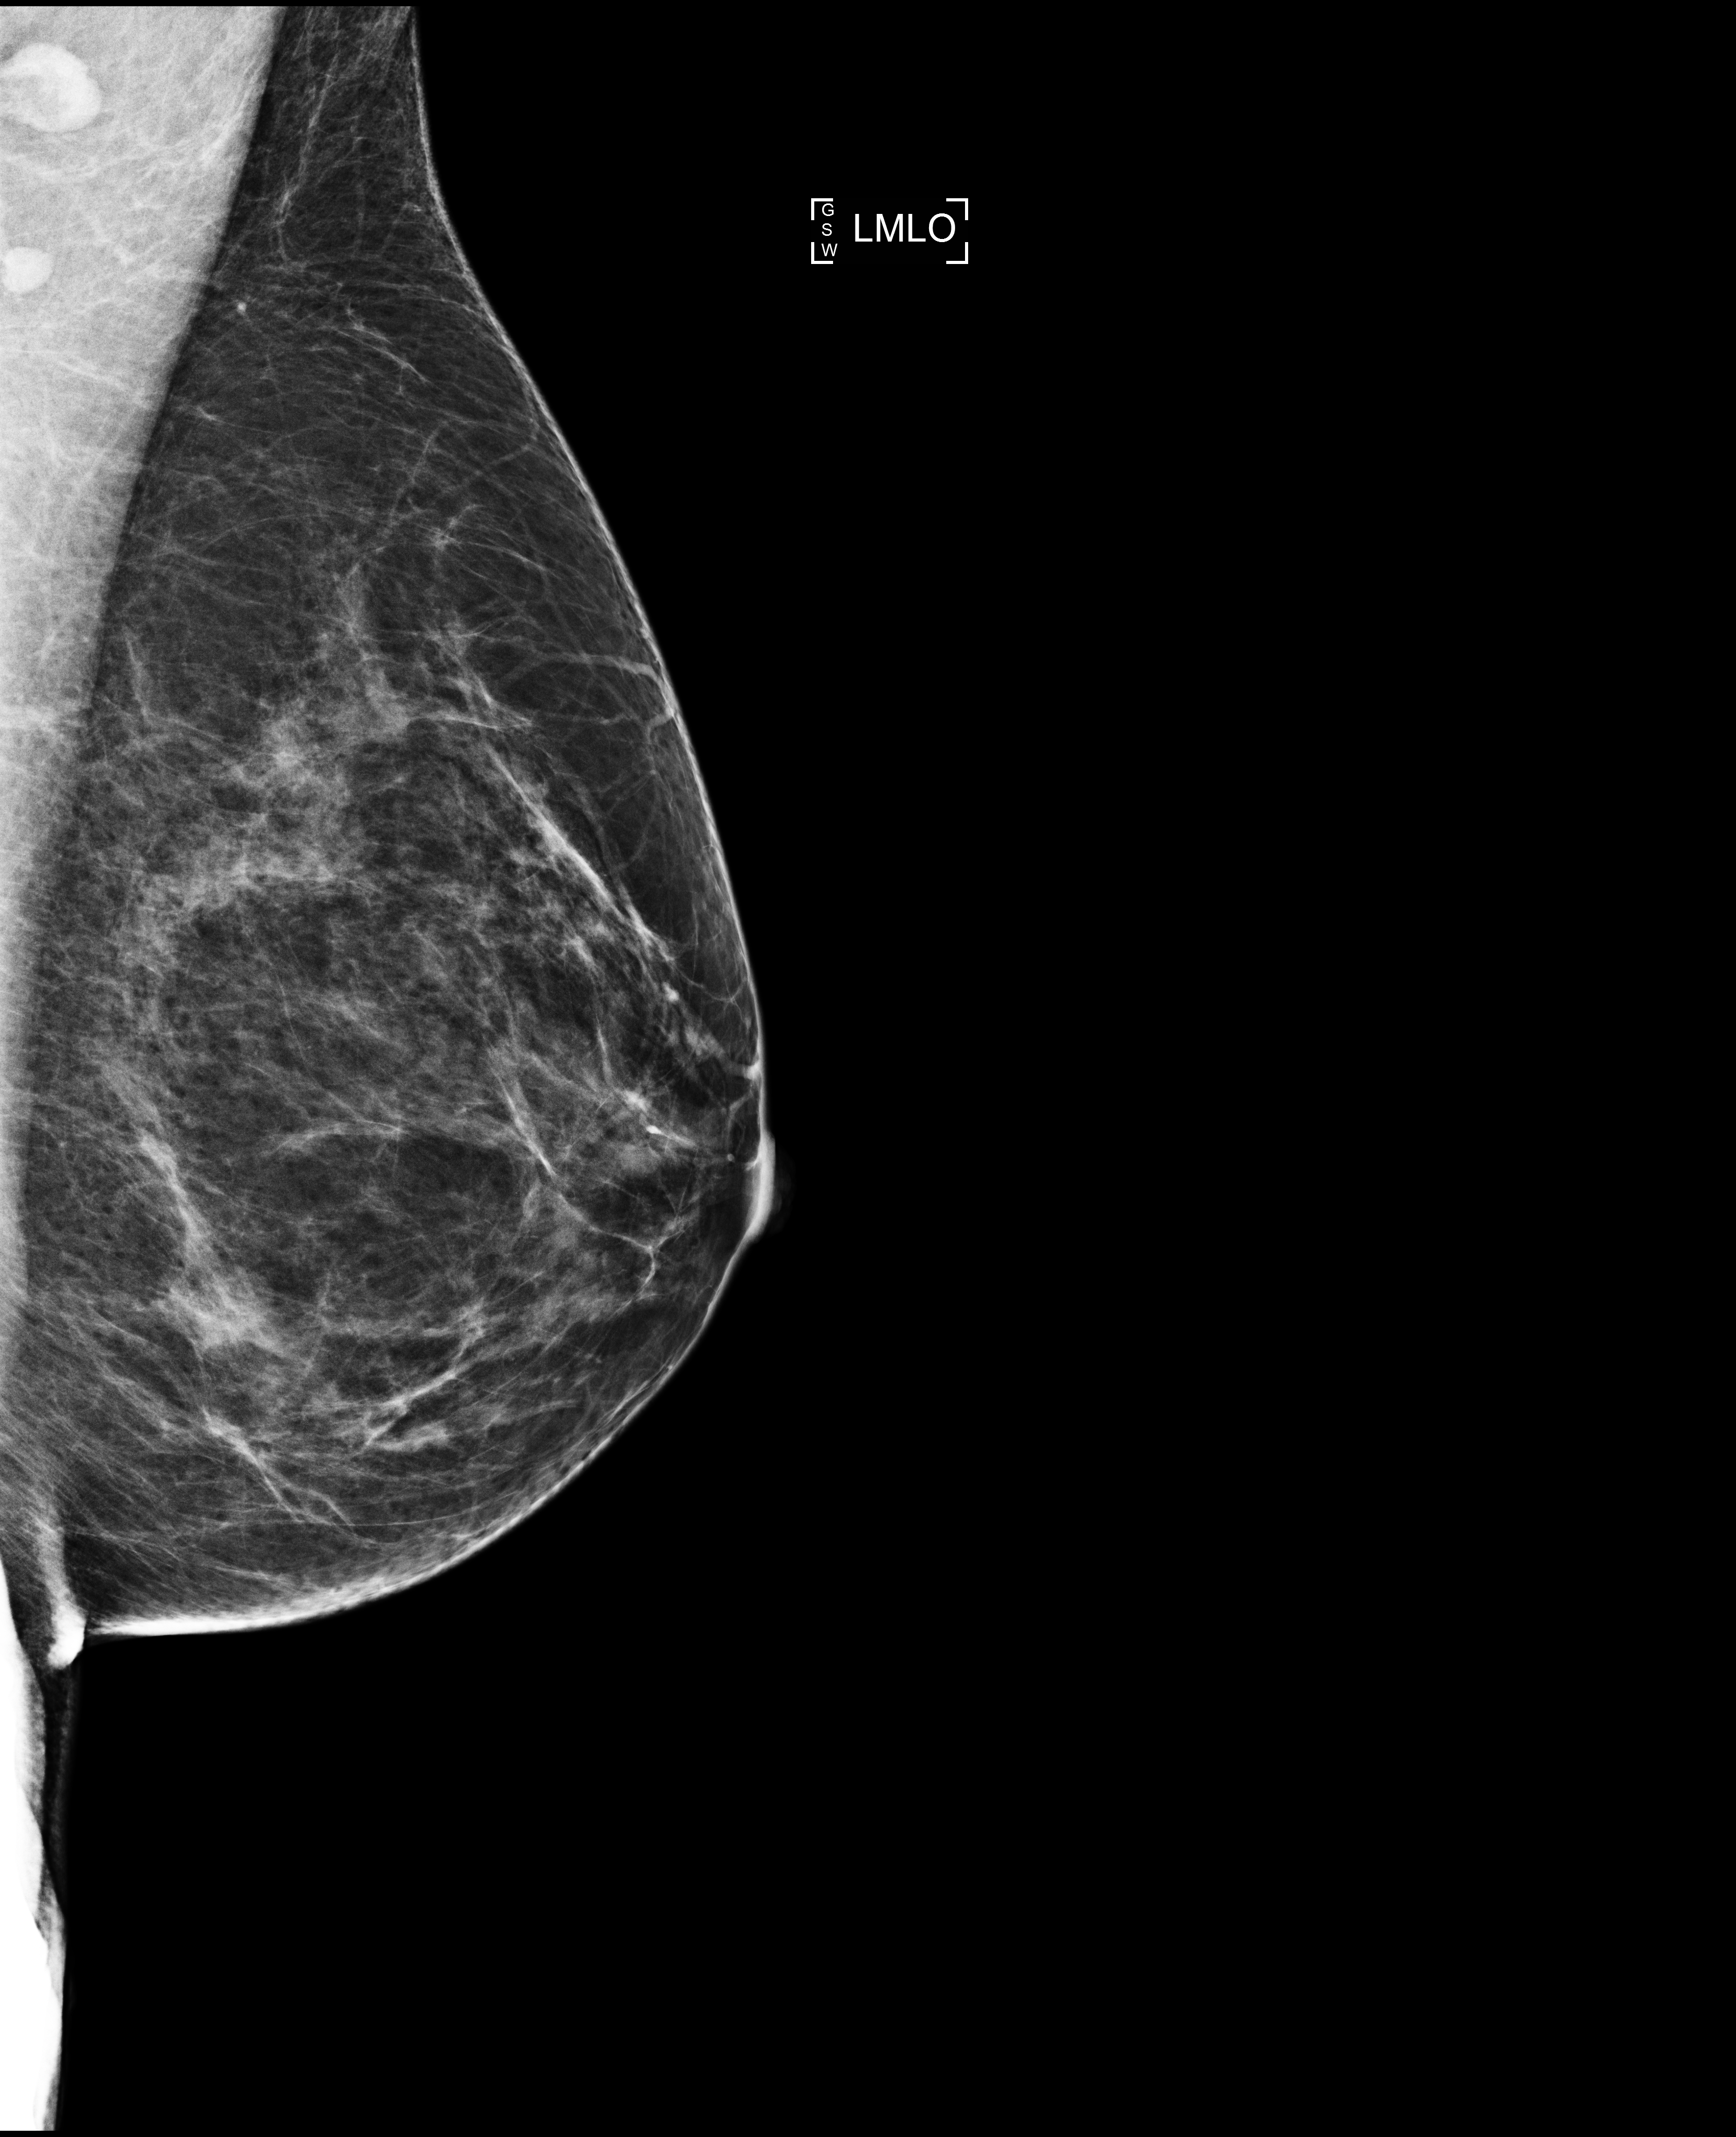
Digital mammogram (FFDM); left breast; medio-lateral oblique projection; screening examination; compressed breast thickness 61 mm. Patient aged 51 years (female).
Breast density at the screening exam (both breasts): heterogeneously dense (BI-RADS density category c). Final BI-RADS category for the screening round (tomosynthesis exam, both breasts): category 1. Recall: no recall after this screen.